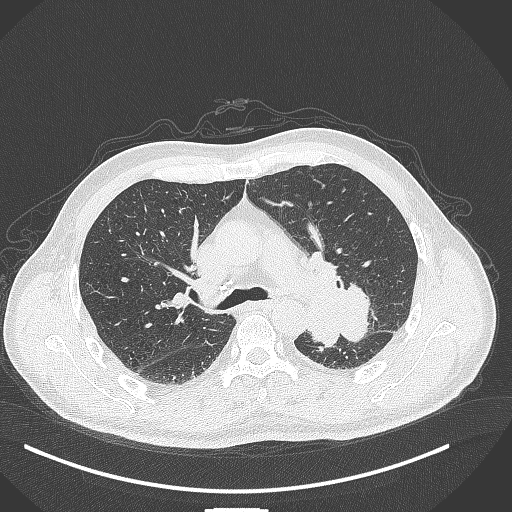
Chest CT, one axial slice. Slice 273 of 429 in the series (ordered by position). 120 kVp. Lung window (W 1500 / L -600 HU). 1 mm slice thickness. 512 × 512 image matrix, field of view 400 × 400 mm. Patient: male, 55 years. From the clinical record (not read from this slice): clinical TNM (as recorded): T3 N0 M1c.
Structures marked on this image (bounding box drawn by a radiologist):
- lung tumour (recorded histology: adenocarcinoma): bounding box [x1, y1, x2, y2] px = [310, 276, 373, 353]